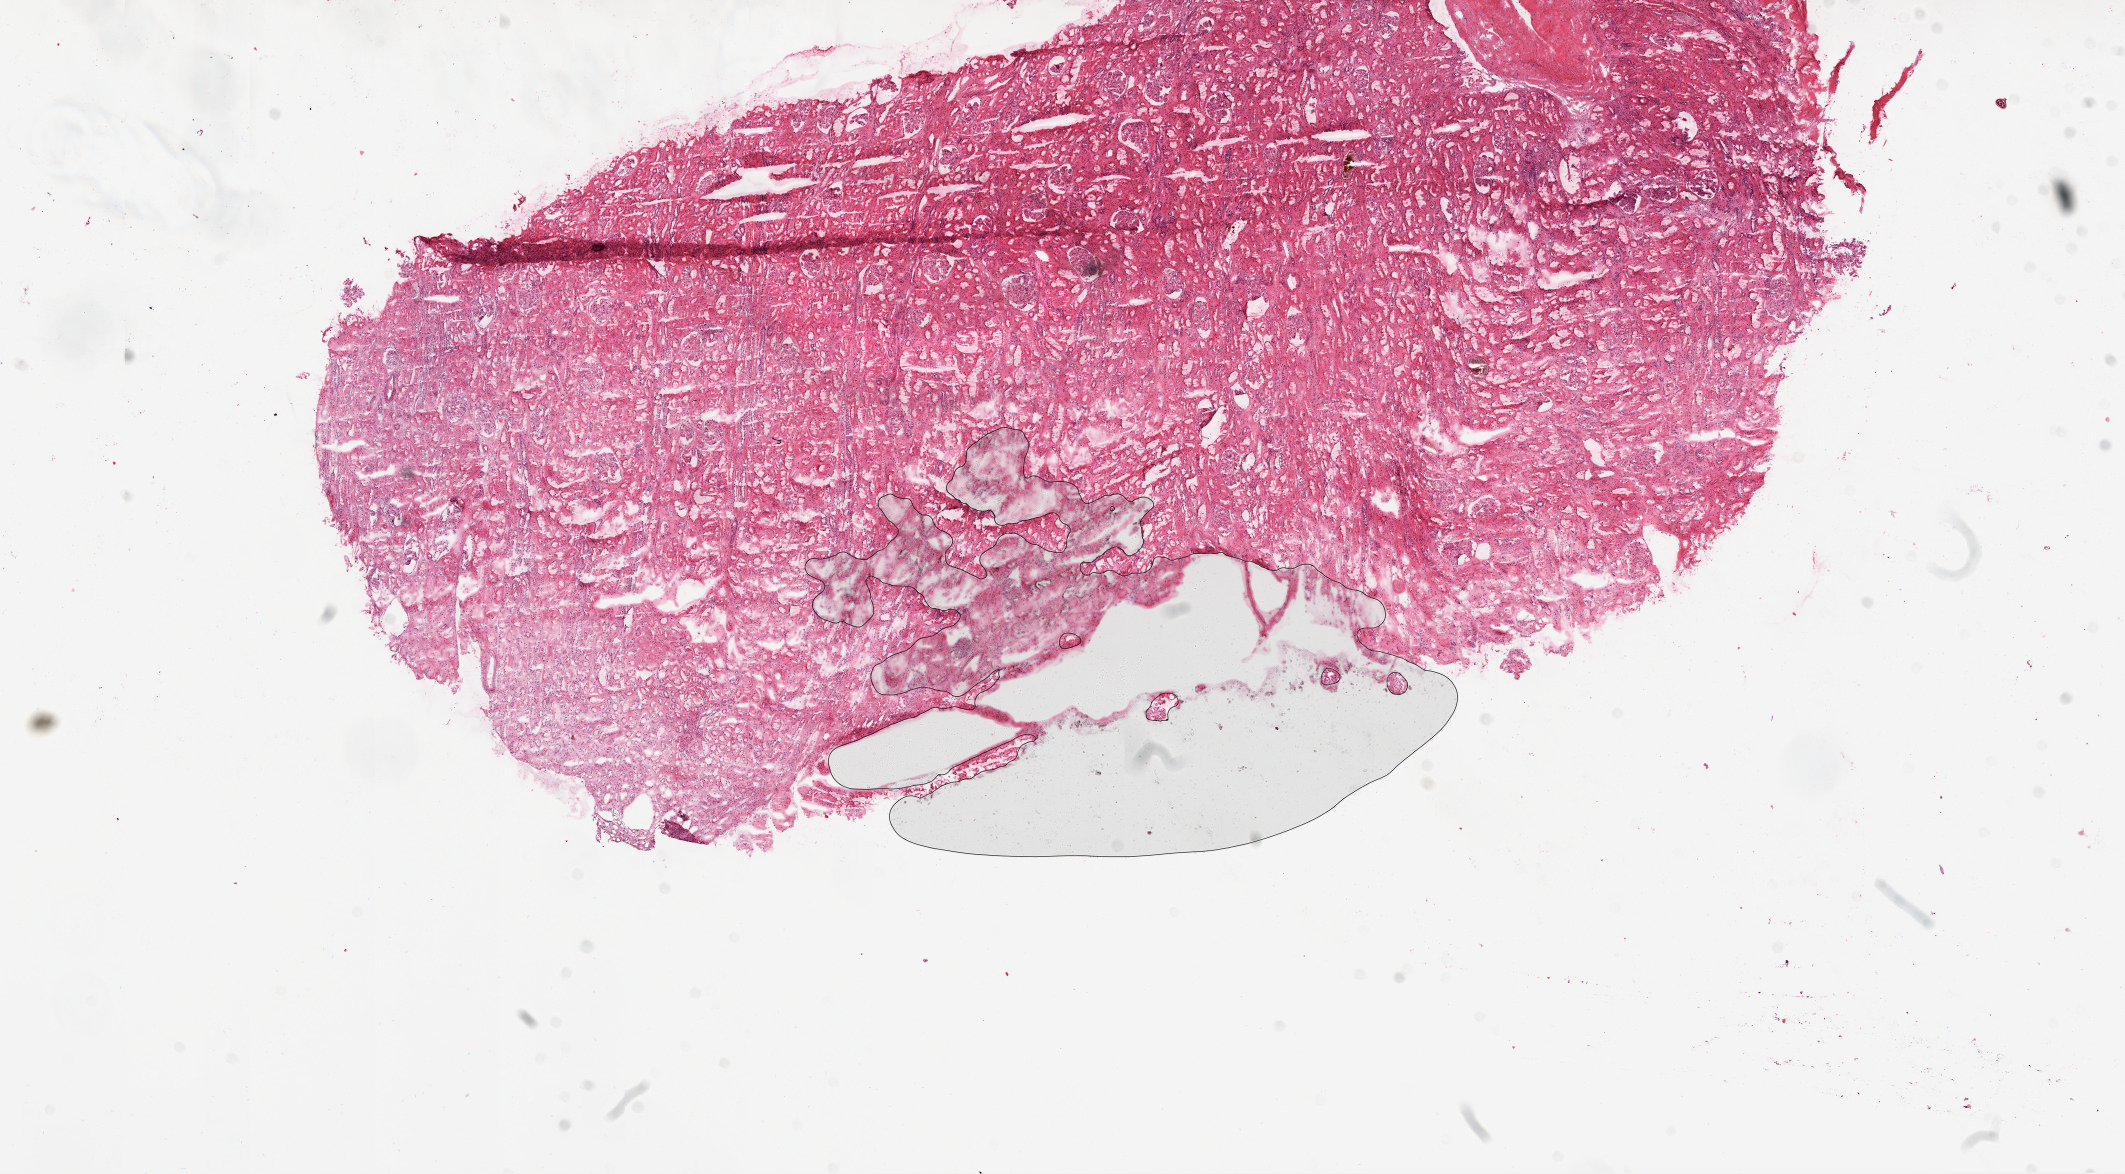
Whole-slide histology image, H&E — low-resolution overview of the scanned area, about 17.1 x 9.4 mm (from a 20x scan); frozen section from the top of the tissue portion; sample: solid tissue normal (non-tumour tissue), kidney. Male, age 71 years at initial diagnosis.
- this section: solid tissue normal sample (biorepository sample class)
- patient diagnosis: Clear cell adenocarcinoma, NOS